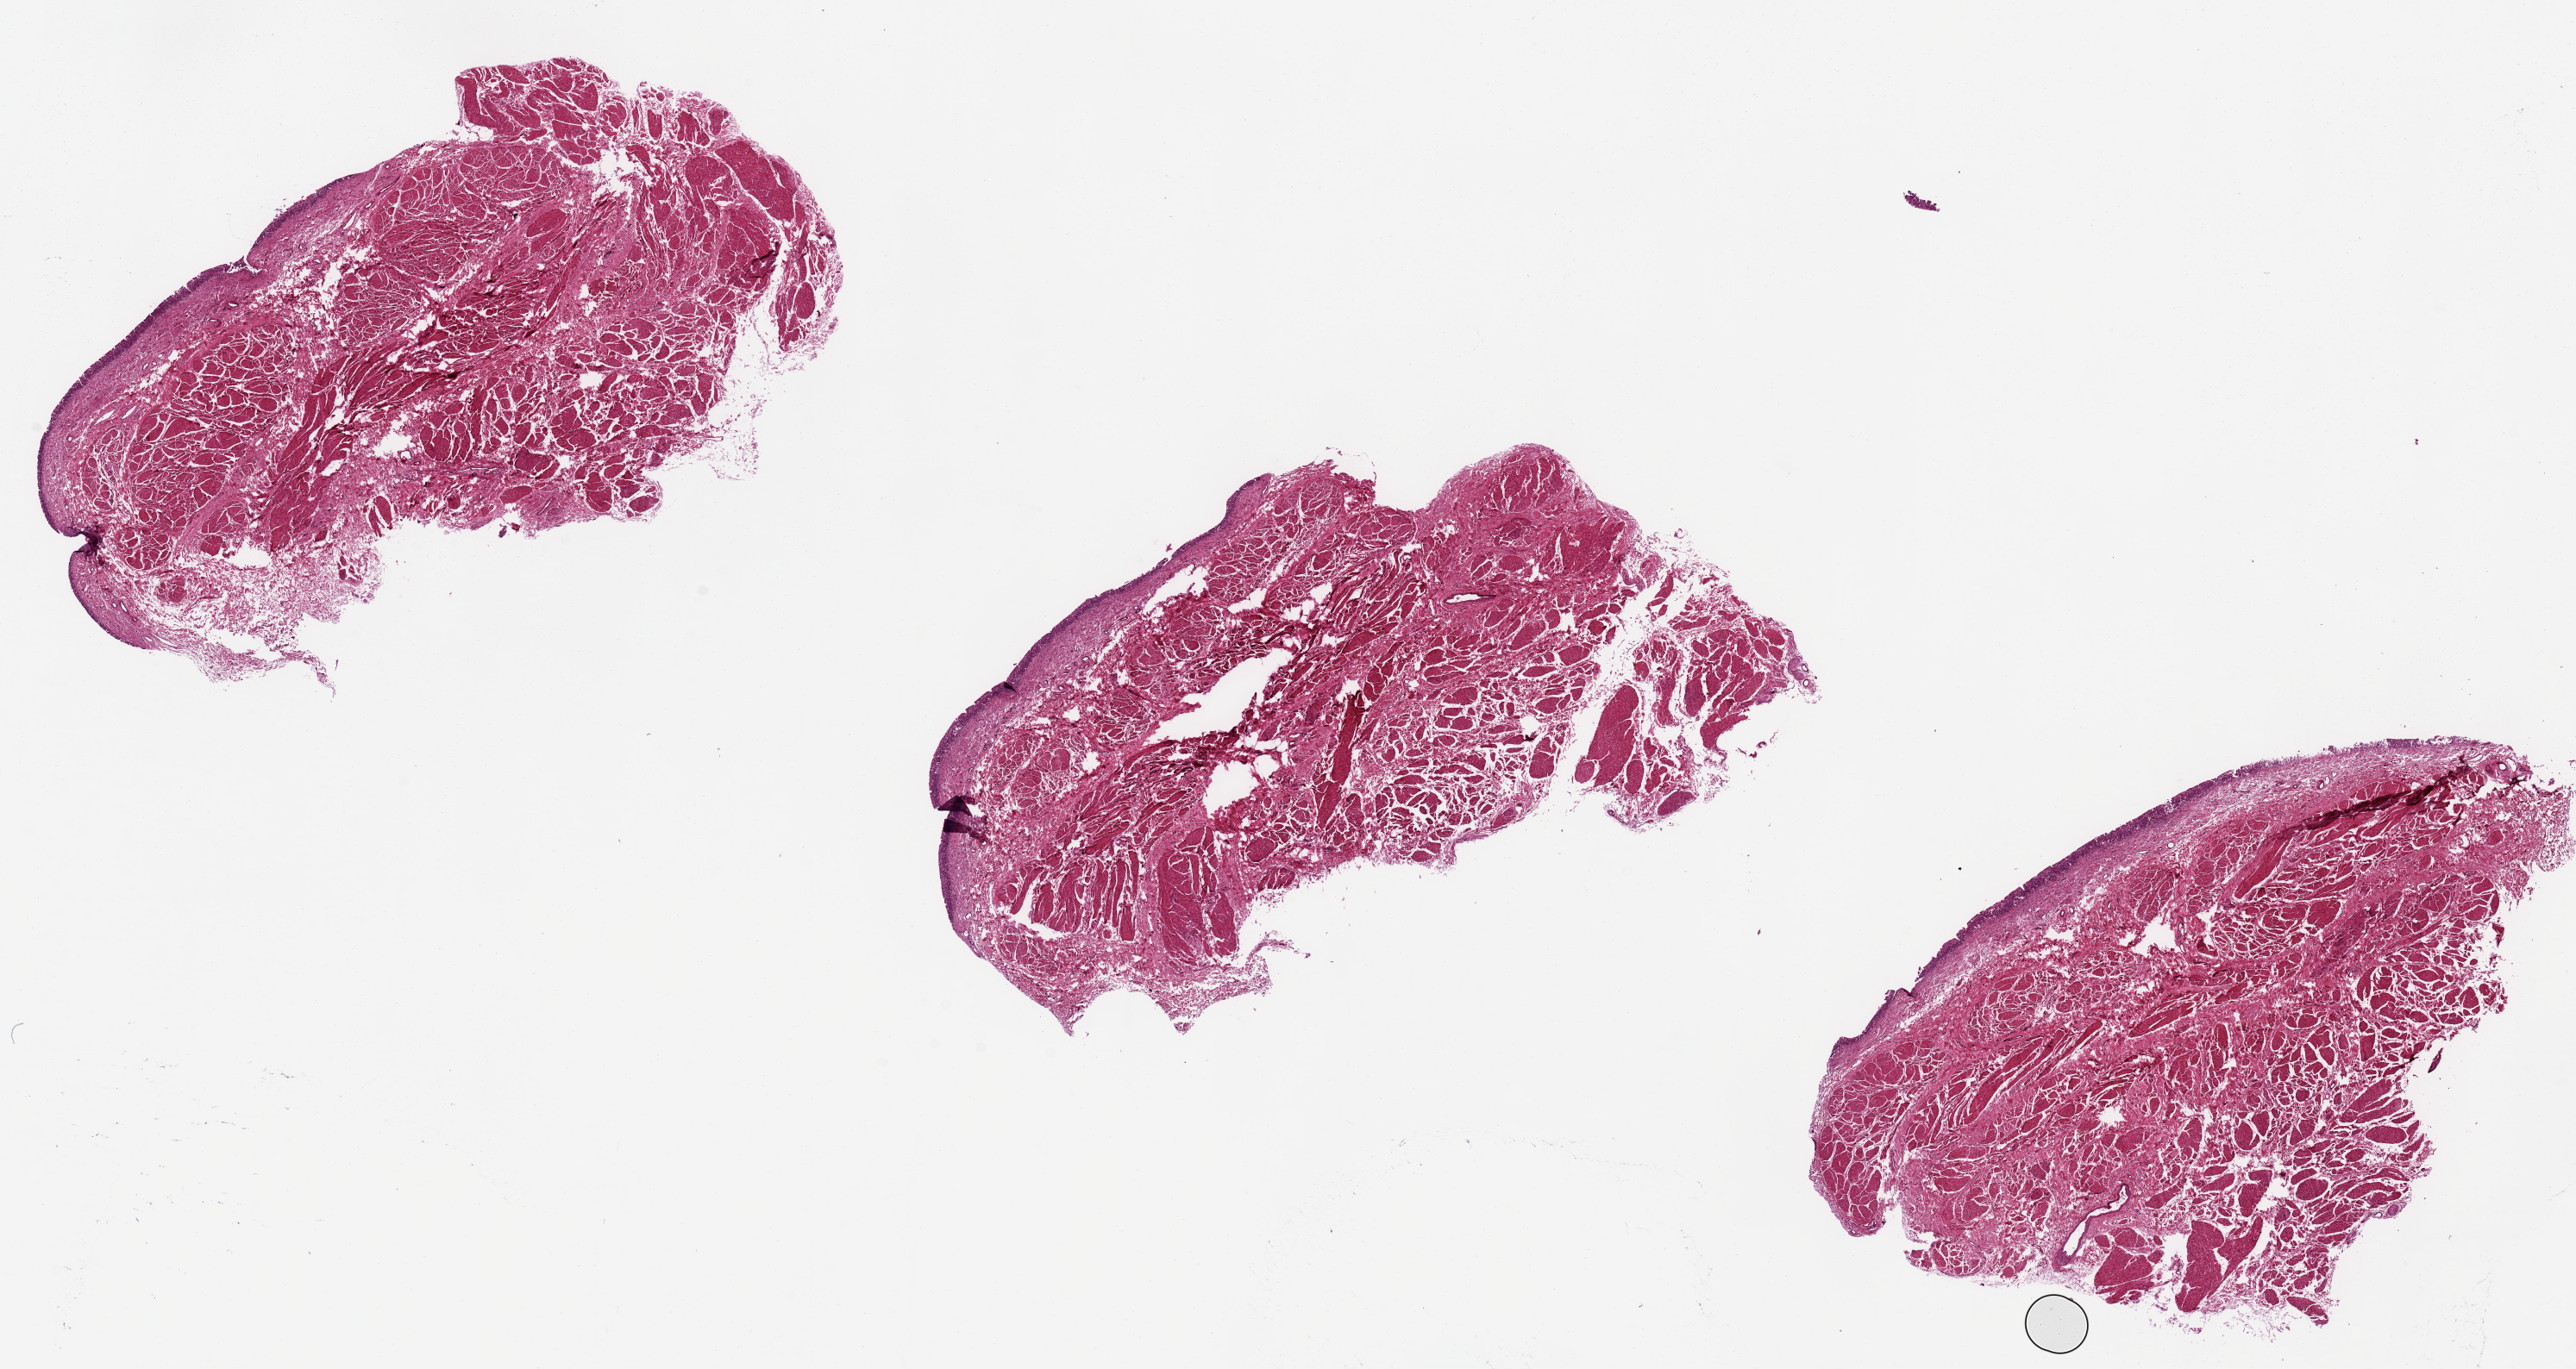
Whole-slide image, H&E stain, low-resolution overview of the scanned area, about 23.6 x 12.6 mm; PAXgene-fixed paraffin-embedded (PFPE) section; target tissue: urinary bladder; donor tissue sample. Female donor.
Reviewer comment on this tissue sample: 3 pieces.